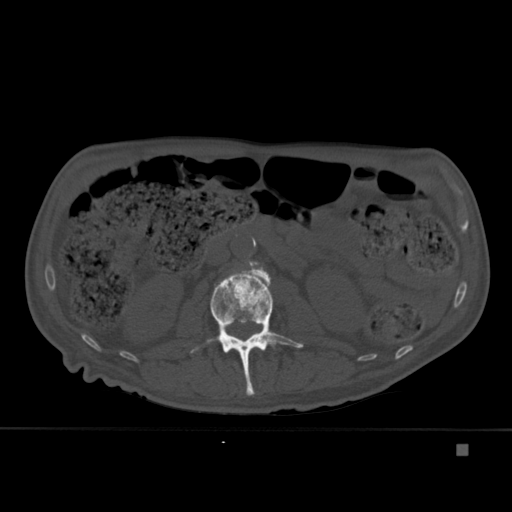
CT including the spine, one axial slice; position 161 of 451 along the scan axis; bone window (W 1800 / L 400 HU); 1.5 mm slice thickness; 512 × 512 image matrix, field of view 378 × 378 mm. Patient: male, 75 years. Case-level facts recorded for this patient, not image findings: primary cancer: prostate.
Outlined on this slice (semi-automatic segmentation, software-assisted and operator-edited):
- L2 vertebra: bounding box <190,264,304,396> (left, top, right, bottom; pixels)
- L3 vertebra: <249,261,259,266>